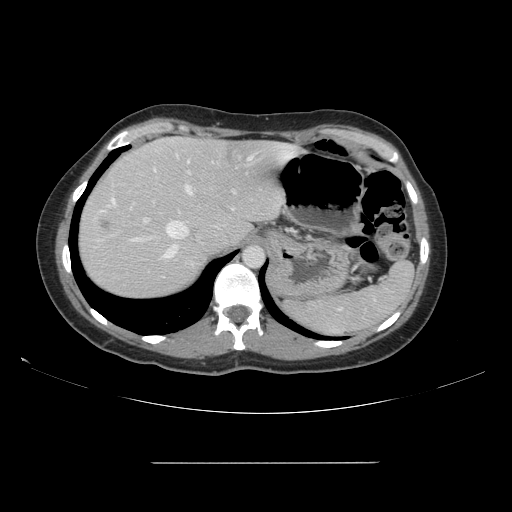
Contrast-enhanced abdominal CT, one axial slice; position 120 of 151 along the scan axis; 120 kVp; soft-tissue window (W 400 / L 40 HU); 2.5 mm slice thickness; 512 × 512 image matrix, field of view 421 × 421 mm. Female patient, age 46 years. Case-level facts recorded for this patient, not image findings: diagnosis: colorectal cancer liver metastases, imaged before liver resection; multiple liver metastases: yes.
Annotated regions visible in this slice (outlined manually by an expert reader):
- hepatic veins: bounding box <111,155,254,257> (left, top, right, bottom; pixels)
- liver: <79,137,296,299>
- planned liver remnant (the part of the liver to remain after resection): <92,137,295,249>
- portal vein (with intrahepatic branches): <166,208,234,257>
- liver metastasis: <99,218,112,231>
- liver metastasis: <226,147,236,162>